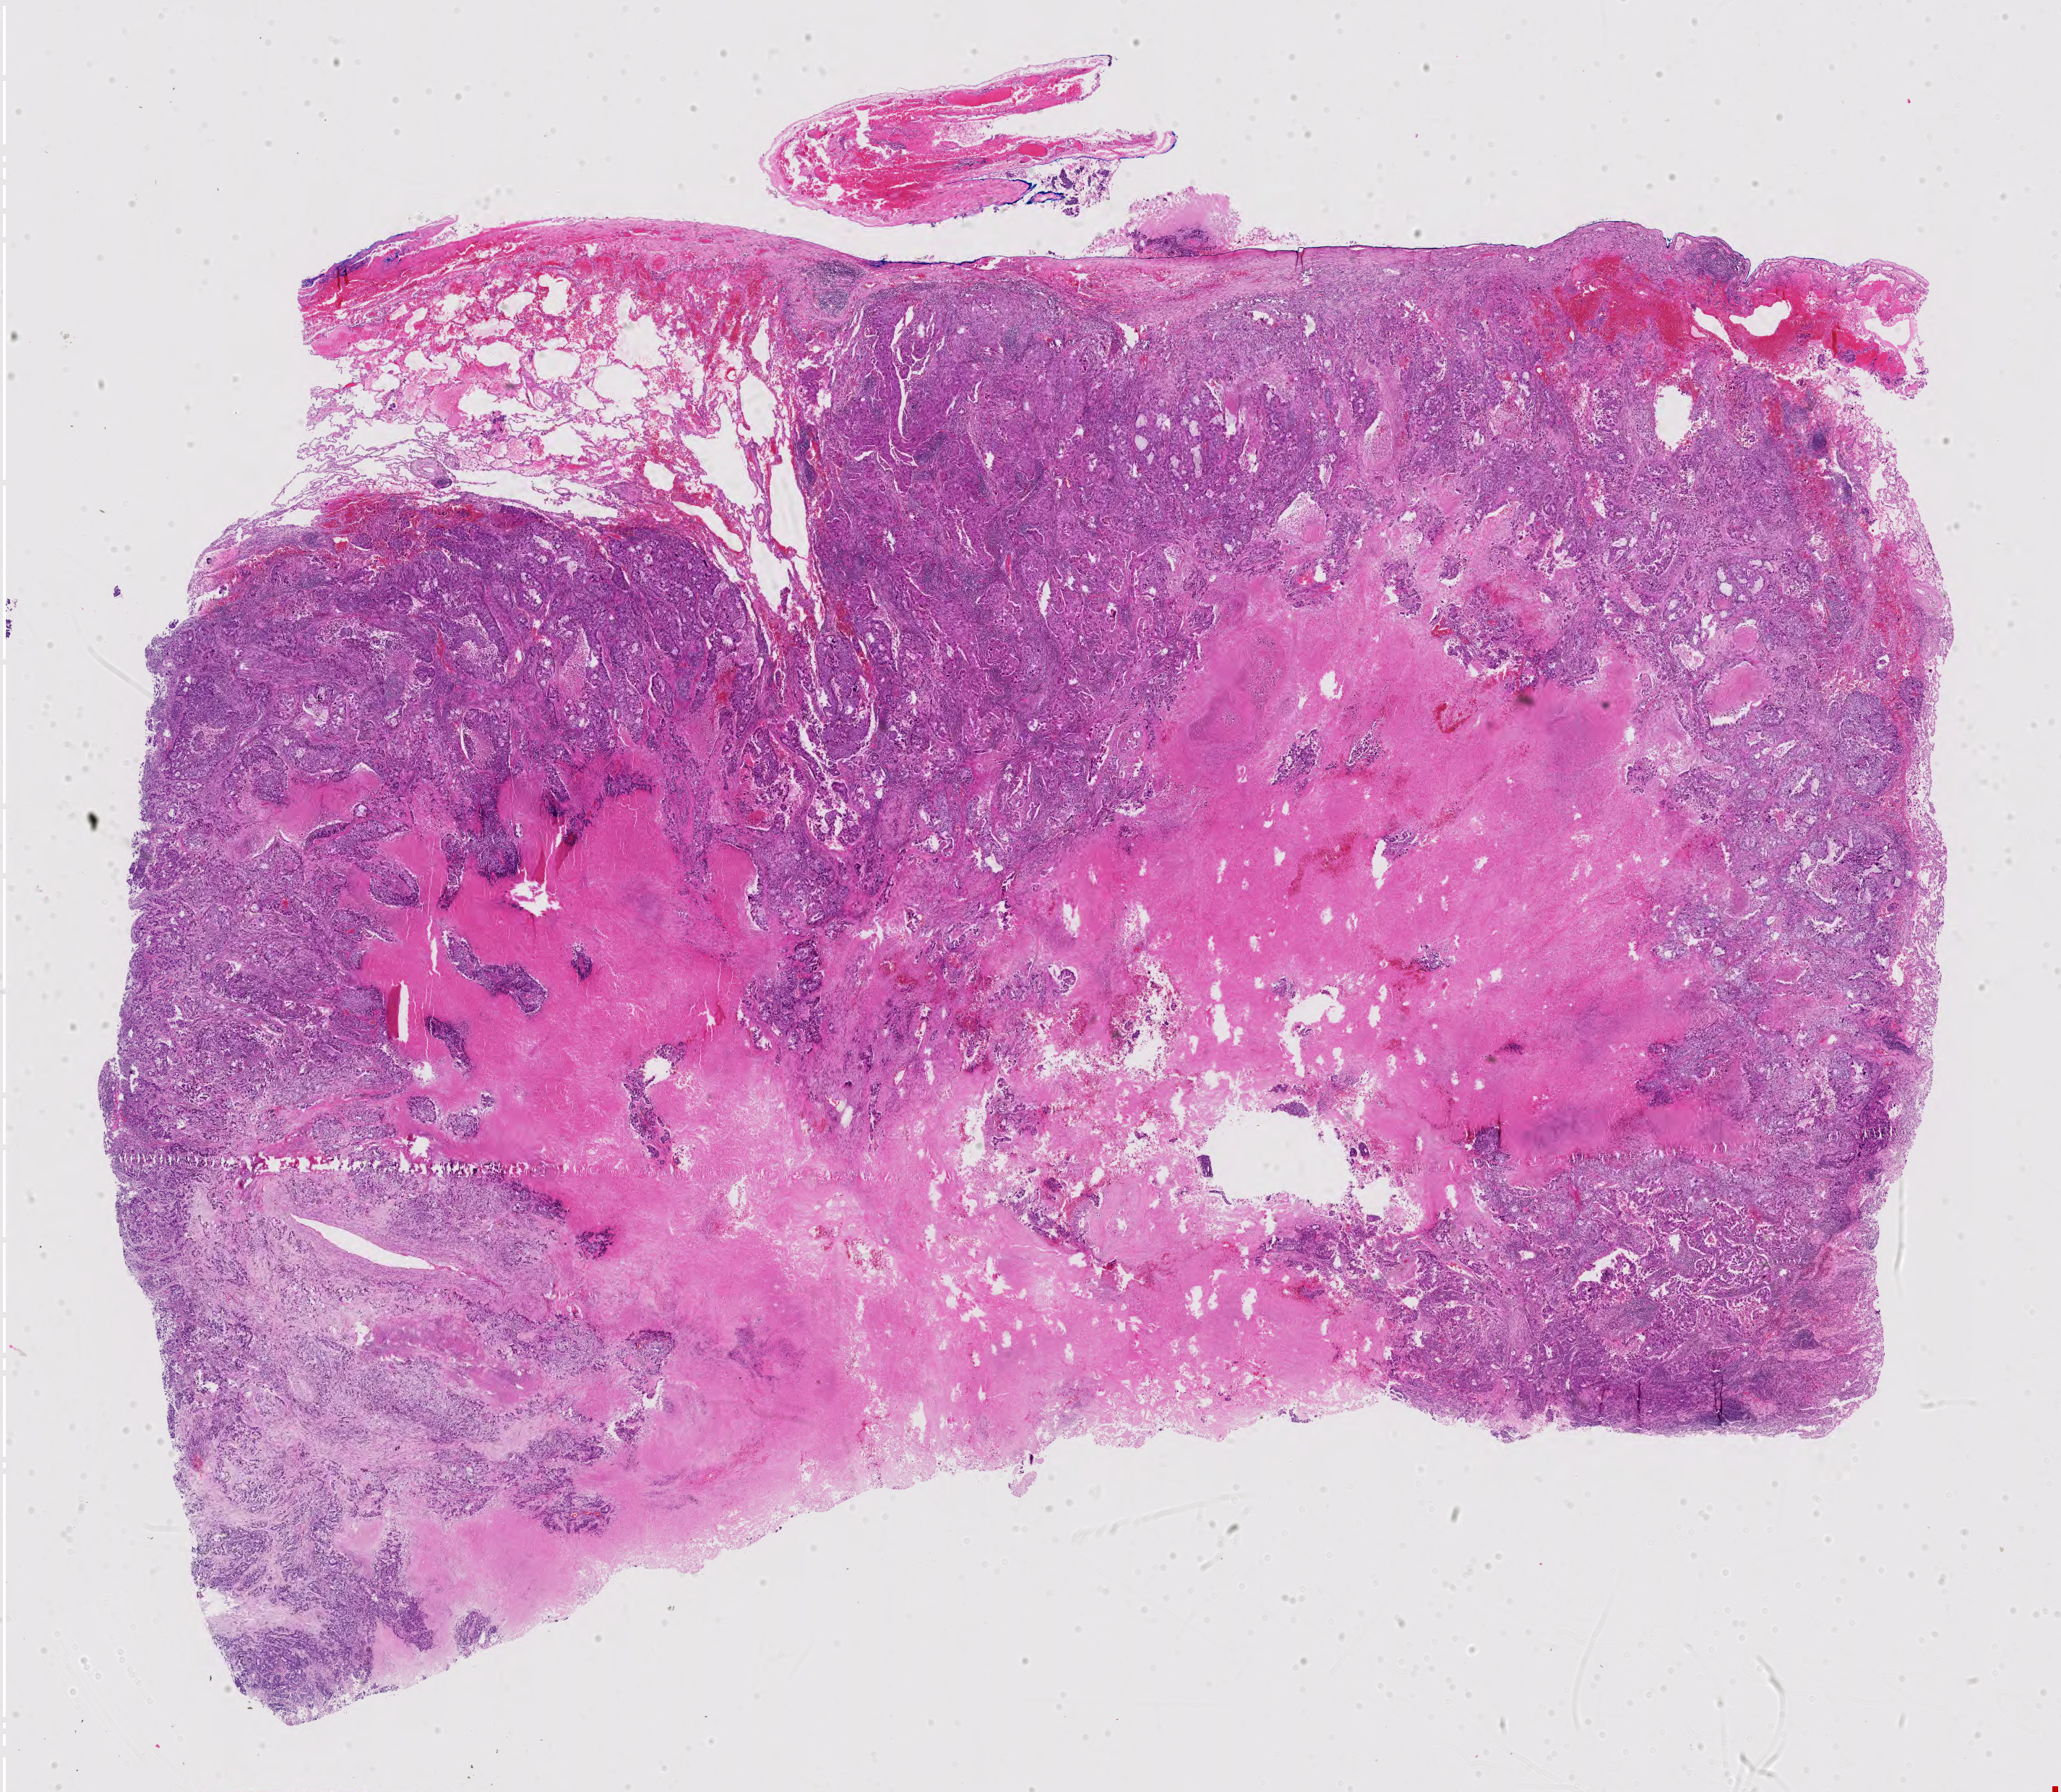
H&E whole-slide image, low-resolution overview of the scanned area, about 20.7 x 18.0 mm (acquisition: 40x scan). FFPE section. Primary tumour sample from the lung. Male patient; age at initial diagnosis 71 years.
Pathologic diagnosis: Adenocarcinoma, NOS (lower lobe, lung). TNM: T2a N1 M0. AJCC pathologic stage: IIA (7th edition).